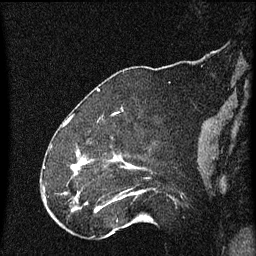
Breast MRI (dynamic contrast-enhanced), one sagittal slice; slice 19 of 60 in the series (ordered by position); dynamic contrast-enhanced series, image 2 of 4 at this slice position (ordered by acquisition); 1.5 T; TE 4.2 ms, TR 8 ms; 2 mm slice thickness; 256 × 256 image matrix, field of view 180 × 180 mm. Female patient, age 52 years.
Structures marked on this image (semi-automatic segmentation, software-assisted and operator-edited):
- analysis volume of interest (the breast-tissue region the enhancement analysis was run in; not a lesion): bounding box (x1, y1, x2, y2) in pixels: (73, 148, 153, 219)
- tumour enhancement mask (voxels above the 70 % enhancement threshold inside the analysis volume of interest): (73, 162, 136, 211)